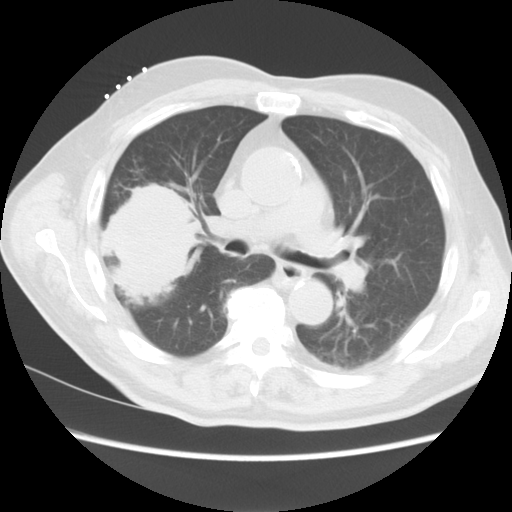
Chest CT, one axial slice. Slice 7 of 15 in the series (ordered by position). Reconstruction kernel STANDARD. 120 kVp. Lung window (W 1500 / L -600 HU). 5 mm slice thickness. 512 × 512 image matrix, field of view 350 × 350 mm. Patient: male, 68 years. Case-level facts recorded for this patient, not image findings: clinical TNM (as recorded): T4 N3 M0.
Outlined on this slice (bounding box drawn by a radiologist):
- lung tumour (recorded histology: squamous cell carcinoma): box from (x=107, y=177) to (x=204, y=303) px